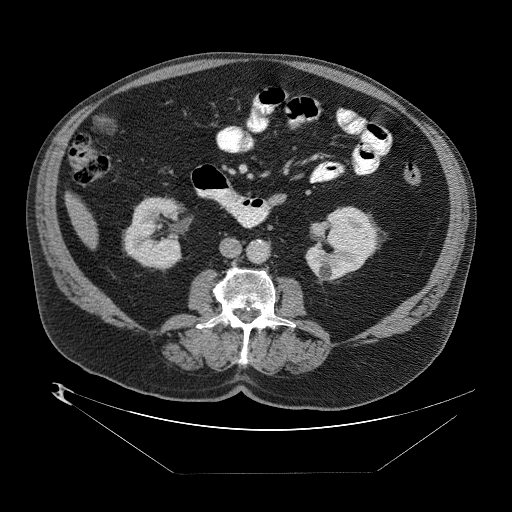
Contrast-enhanced abdominal CT (liver protocol), one axial slice; reconstruction kernel STANDARD; 140 kVp; one of 2 acquisitions stored at this slice position; soft-tissue window (W 400 / L 40 HU); 512 × 512 image matrix, field of view 480 × 480 mm. Case-level facts recorded for this patient, not image findings: diagnosis: hepatocellular carcinoma (patient treated with transarterial chemoembolisation; whether this scan precedes or follows treatment is not stated here); TNM stage (as recorded): Stage-II; Child-Pugh class: B; tumour differentiation: moderately differentiated; tumour nodularity: multinodular.
Annotated regions visible in this slice (semi-automatically segmented with operator editing):
- abdominal aorta: bounding box (x1, y1, x2, y2) in pixels: (246, 240, 269, 265)
- liver parenchyma outside the tumour (the mass and vessels are separate outlines, so this box may not span the whole liver): (63, 184, 96, 234)